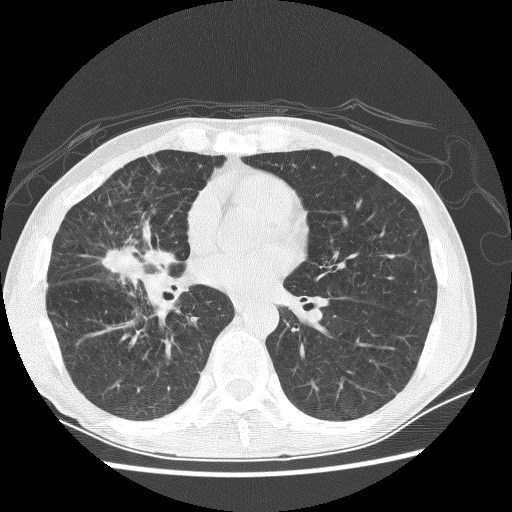
Low-dose screening chest CT, axial slice; first (baseline) screen; lung window (W 1500 / L -600 HU); 2.5 mm slice thickness; lung (sharp) reconstruction kernel (BONE); 120 kVp; slice 135 of 256 in the series. Male participant, aged 67 years at enrolment. Current smoker at enrolment.
Expert-annotated lung lesion, bounding box (x1, y1, x2, y2) in pixels: (78, 223, 173, 295). The exam's reader record, not a measurement of the box and not confirmed to be the same lesion: non-calcified nodule or mass ≥4 mm, right middle lobe, 28 × 18 mm, spiculated (stellate) margins, soft tissue attenuation. Participant outcome: lung cancer diagnosed 69 days after this screen — adenocarcinoma, NOS, right middle lobe, stage IV (AJCC 6th edition), 60 mm at pathology.